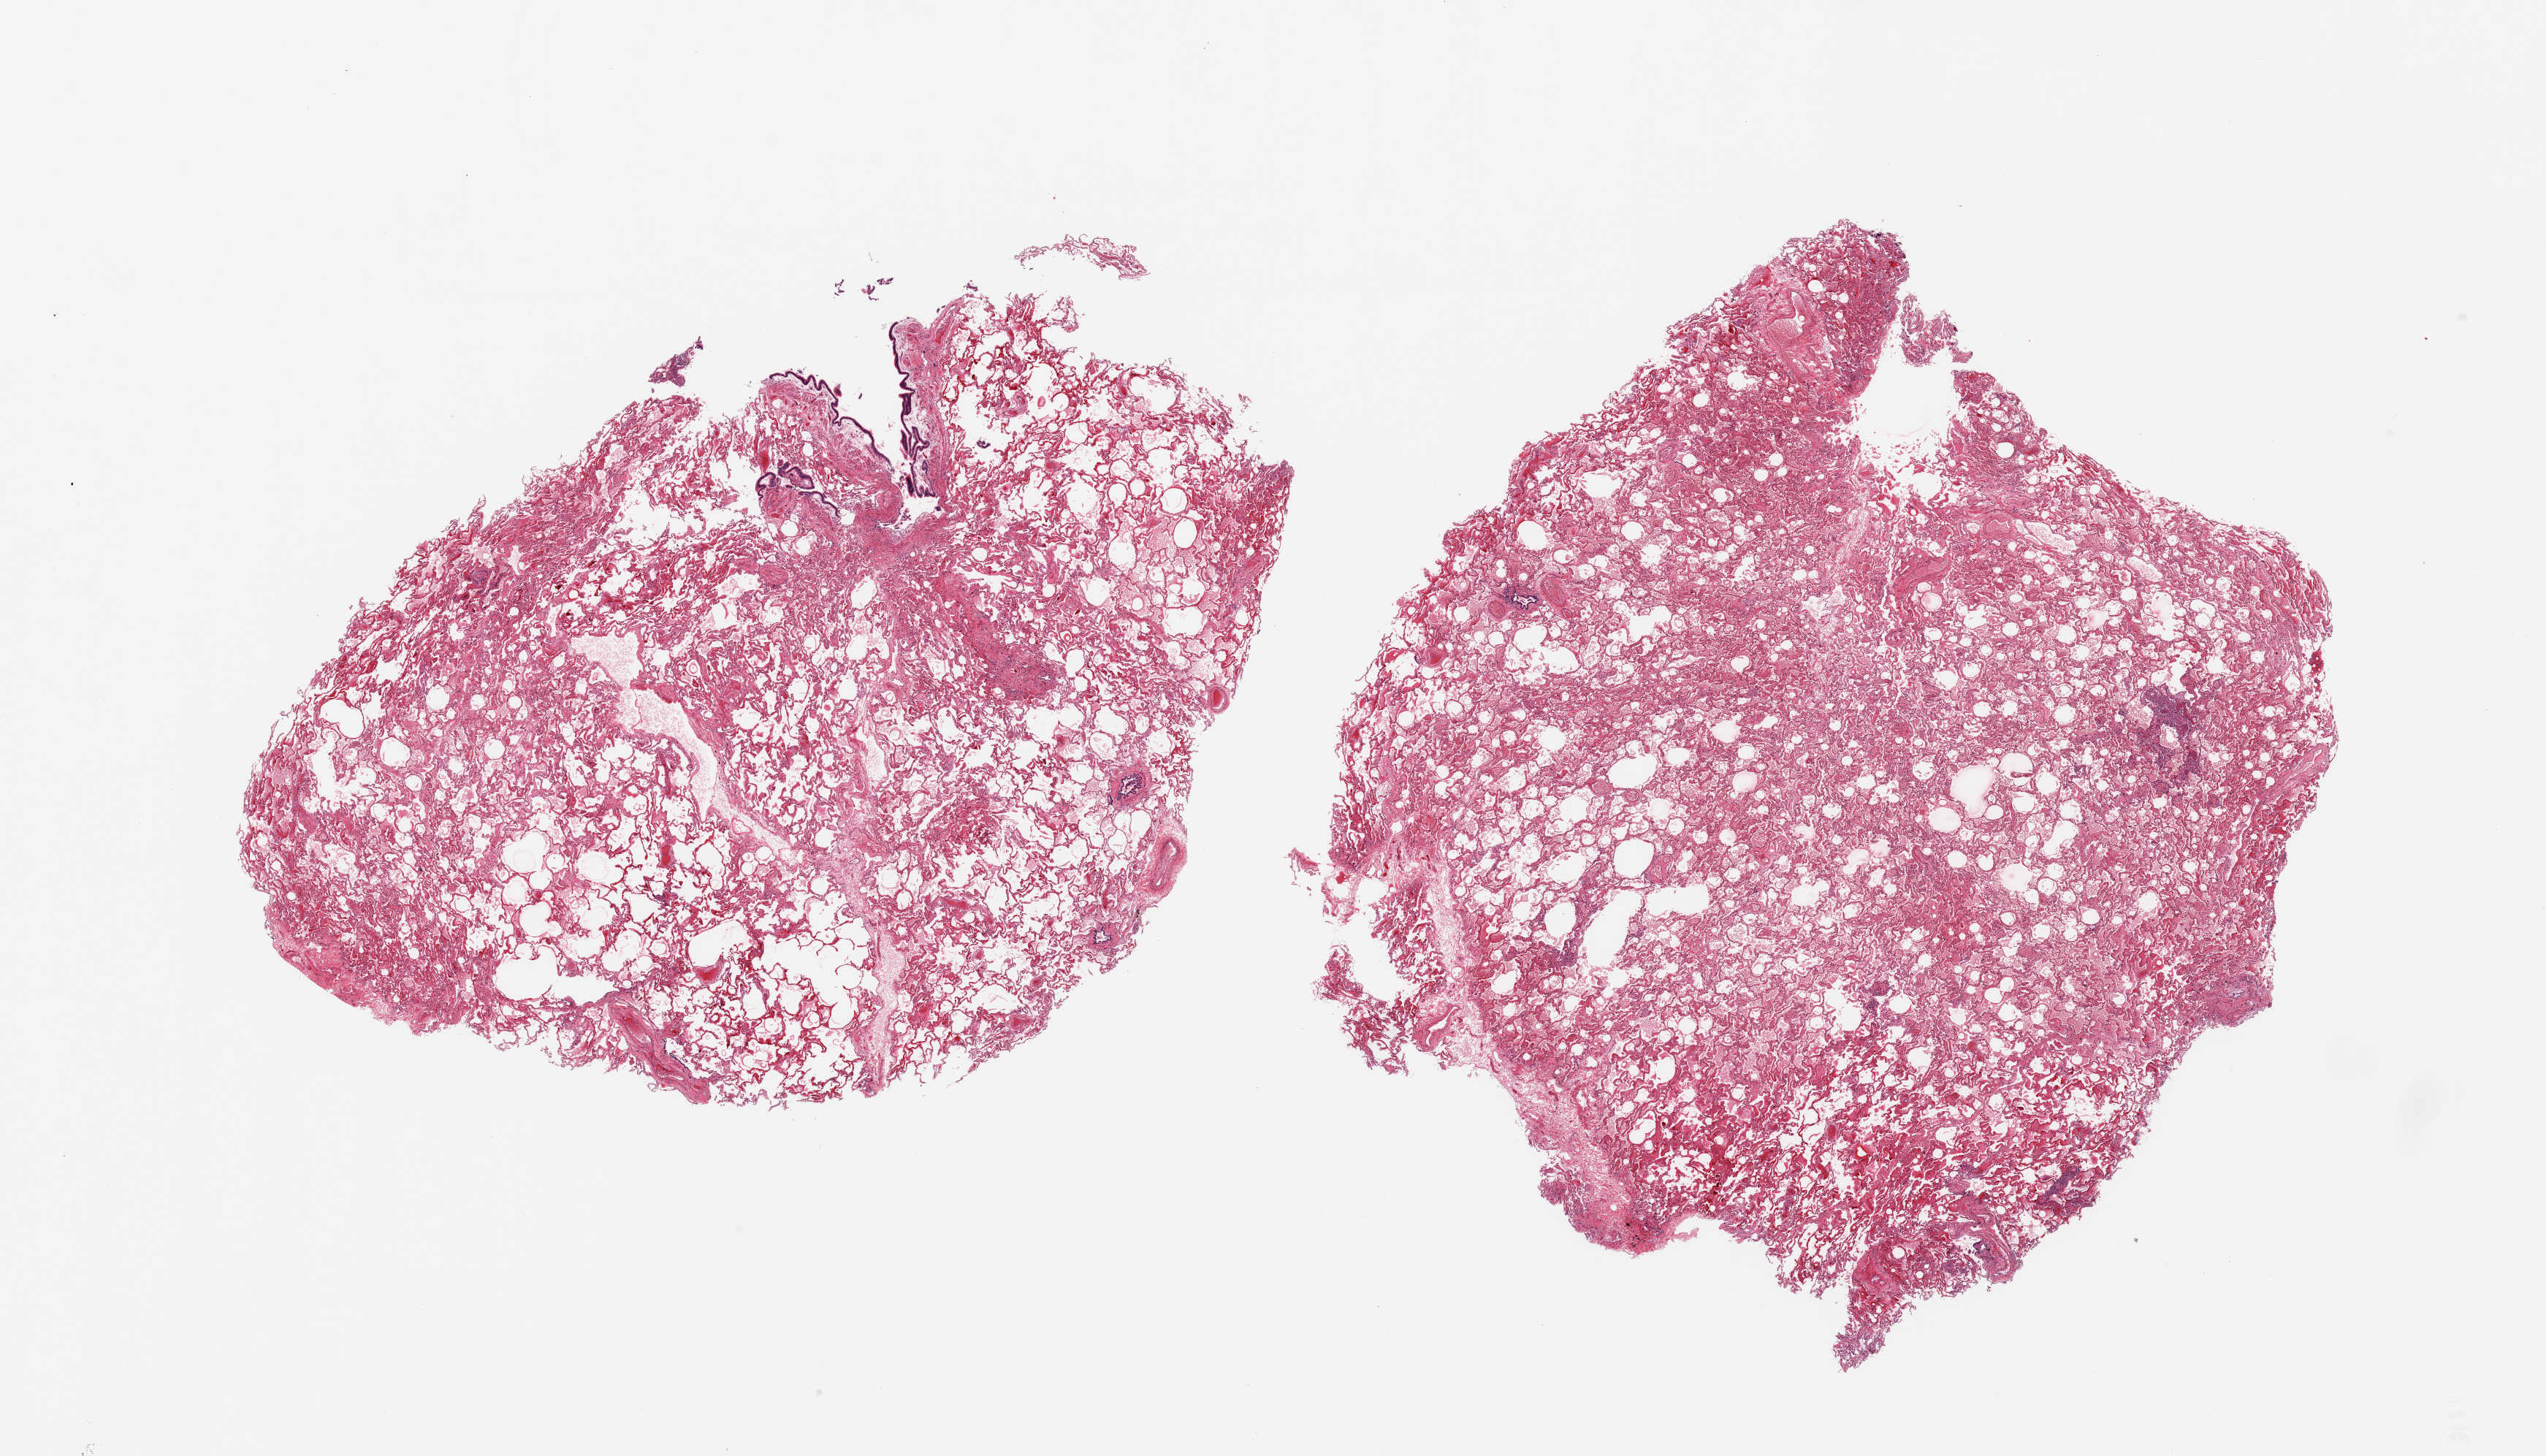
Hematoxylin and eosin (H&E) whole-slide image, brightfield — shown as a low-resolution overview of the whole scanned area (about 27.6 x 15.8 mm); PAXgene-fixed paraffin-embedded (PFPE) section; sampled site (target tissue): lung; donor tissue sample. Donor: male.
Reviewer comment on this tissue sample: 2 pieces; congestion, edema, focal perivascular inflammatory cell infiltrate.